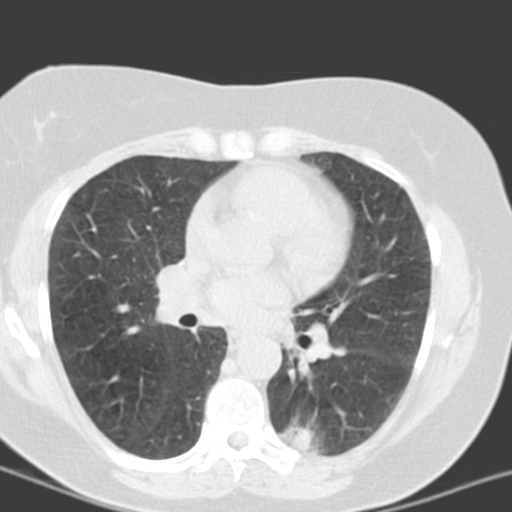
Low-dose screening chest CT, one axial slice. Position 86 of 150 along the scan axis. 120 kVp. Lung window (W 1500 / L -600 HU). 3.2 mm slice thickness. 512 × 512 image matrix, field of view 290 × 290 mm.
Annotated regions visible in this slice (manually delineated by an expert):
- lesion 2 (tumor, lower lobe of left lung): bounding box [x1, y1, x2, y2] px = [288, 427, 314, 451]